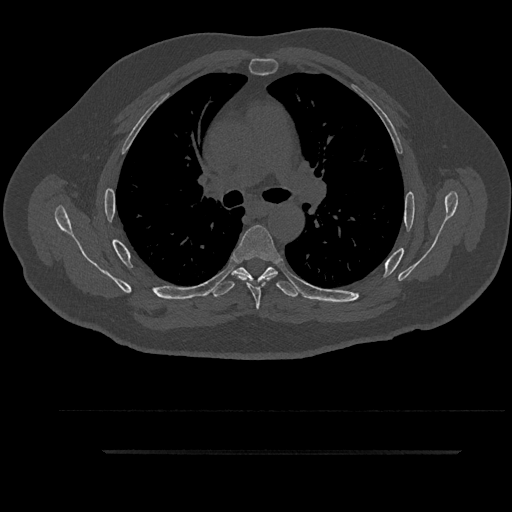
CT including the spine, one axial slice. Slice 609 of 797 in the series (ordered by position). Reconstruction kernel Br40s/3. 120 kVp. Bone window (W 1800 / L 400 HU). 0.5 mm slice thickness. 512 × 512 image matrix, field of view 432 × 432 mm. Male patient, age 63 years. Case-level facts recorded for this patient, not image findings: primary cancer: renal; vertebrae with lytic lesions (as recorded): T8.
Structures marked on this image (semi-automatic segmentation, software-assisted and operator-edited):
- T5 vertebra: bounding box <233,225,282,309> (left, top, right, bottom; pixels)
- T6 vertebra: <212,267,300,297>